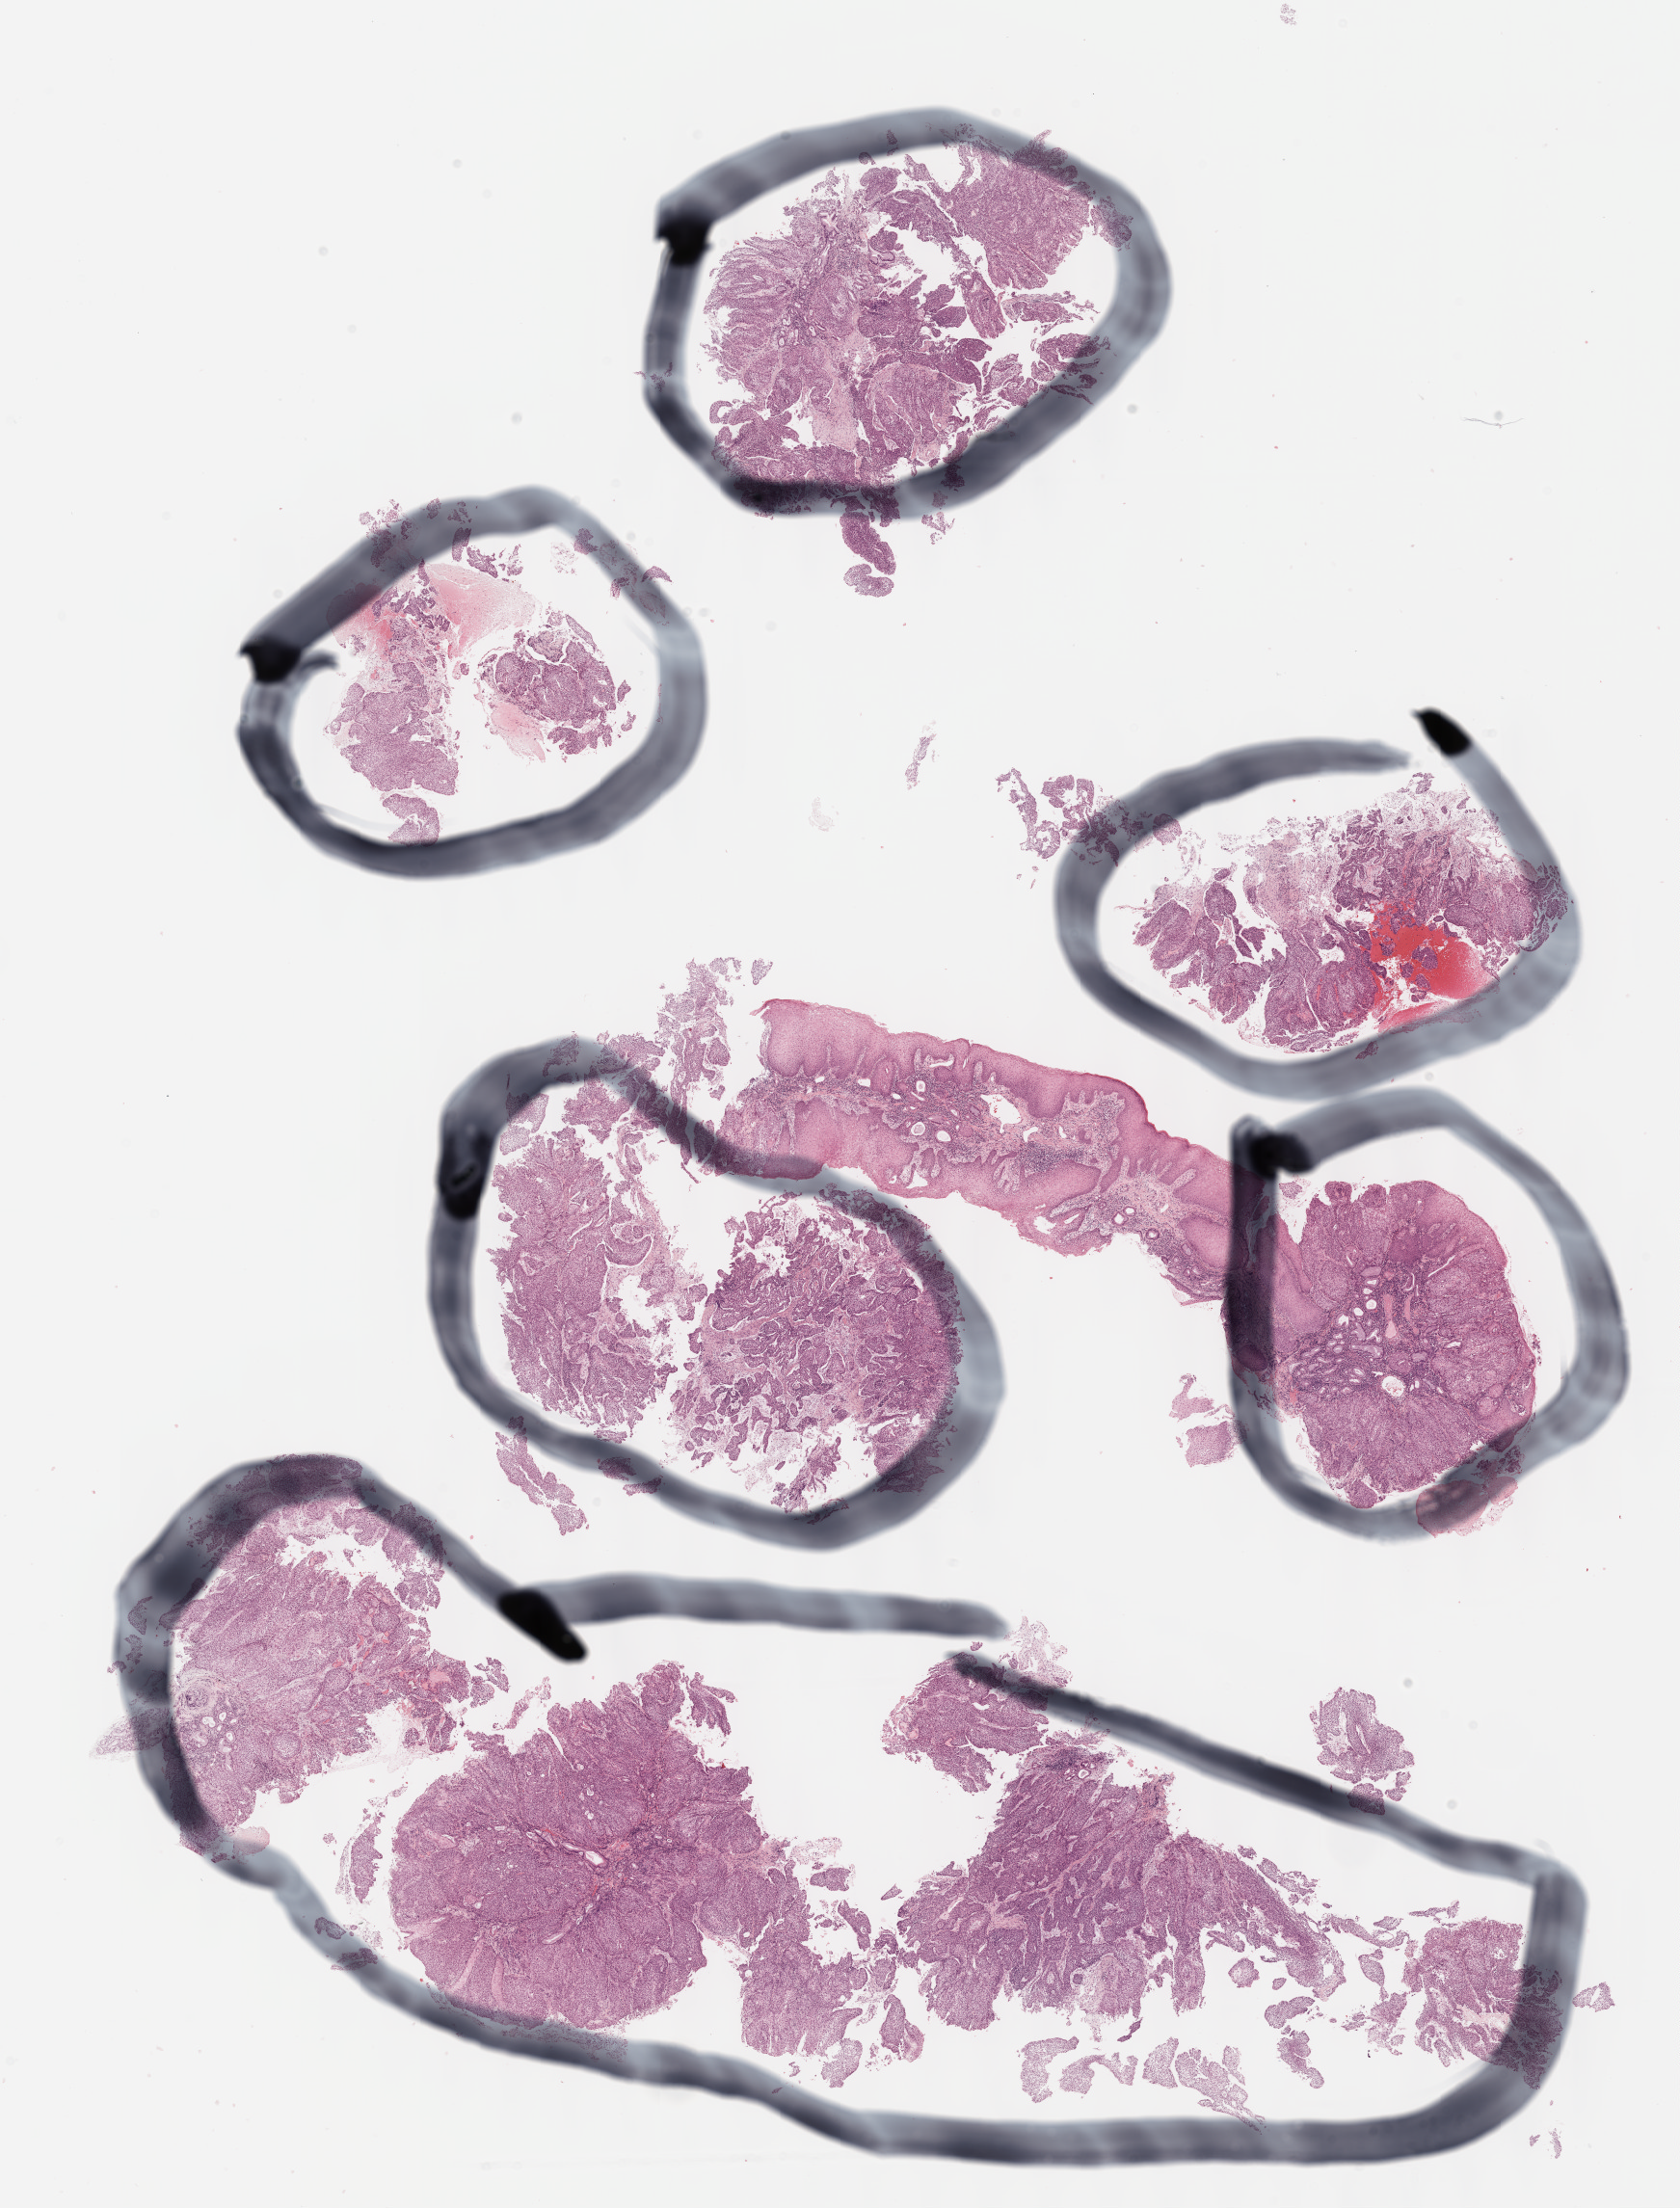
H&E-stained whole-slide image, whole scanned area (about 14.1 x 18.5 mm, from a 40x scan) shown as a low-resolution overview. Formalin-fixed paraffin-embedded (FFPE) diagnostic section. Primary tumour sample from the head and neck. Male, age 53 years at initial diagnosis. Histologic grade: G3 (poorly differentiated).
Pathologic diagnosis: Squamous cell carcinoma, NOS (larynx, NOS).